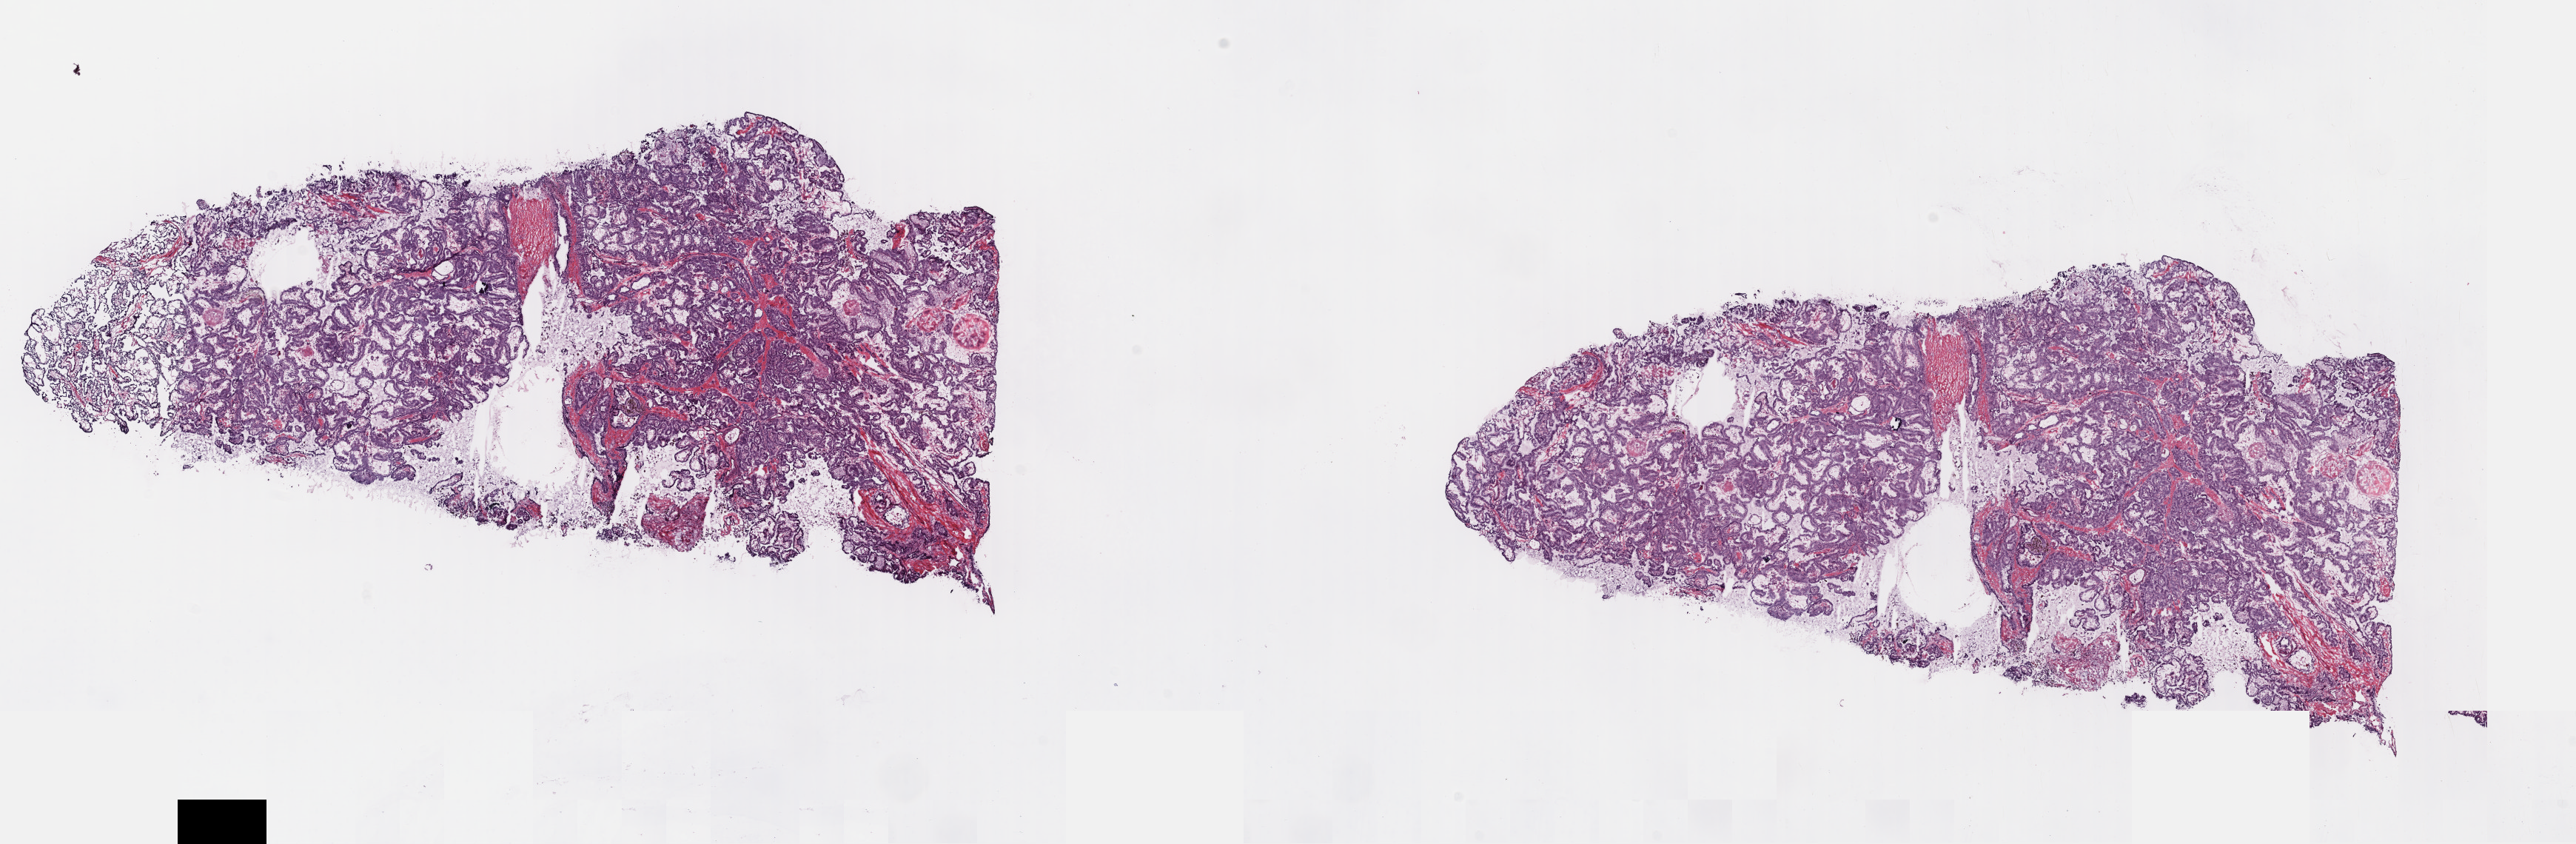
Digitized H&E tissue section (whole slide) — shown as a low-resolution overview of the whole scanned area (about 27.4 x 9.0 mm, from a 40x scan); frozen section from the top of the tissue portion; metastatic tumour sample, sampled site not recorded. Male patient; age at initial diagnosis 39 years. Pathologist review of this section (percent, as recorded): tumour cells 90%, tumour nuclei 85%, normal cells 0%, stromal cells 10%, necrosis 0%. Infiltration values recorded for this section: lymphocyte infiltration 2%, monocyte infiltration 0%, neutrophil infiltration 0%.
• this section: metastatic tumour tissue
• patient diagnosis: Papillary adenocarcinoma, NOS (primary site: thyroid gland)